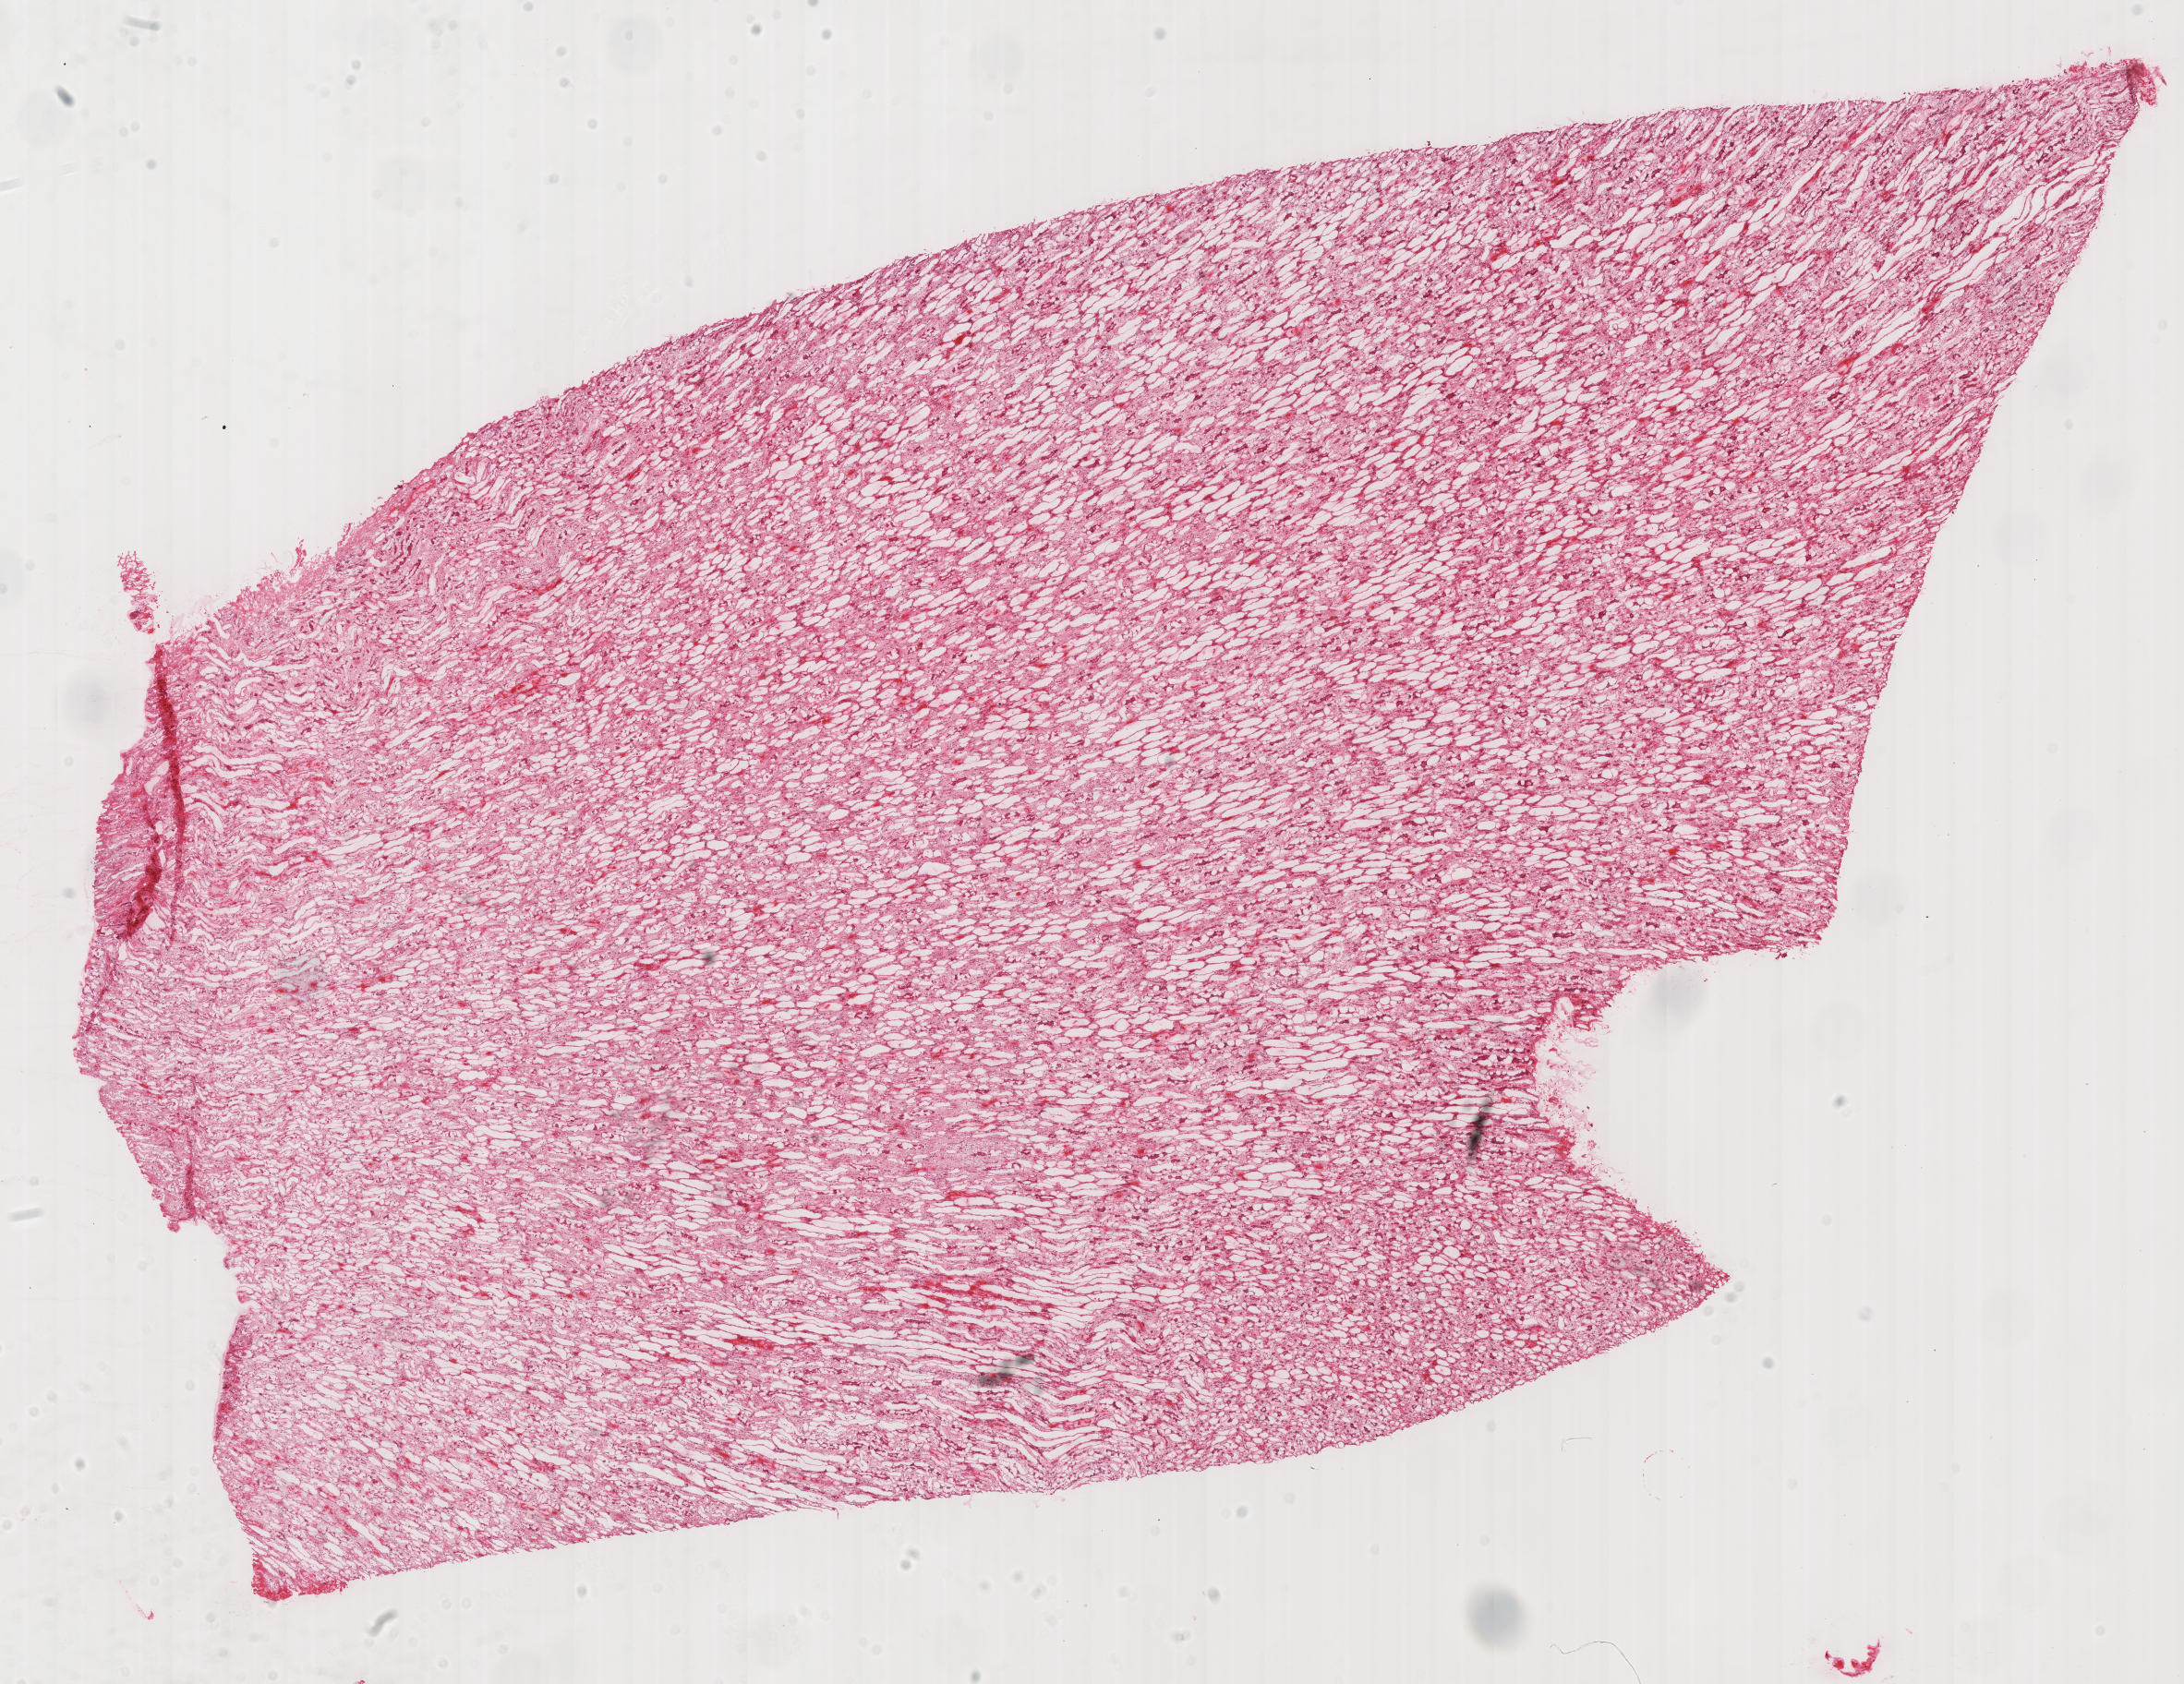
Whole-slide histology image, H&E-stained, low-resolution overview of the scanned area, about 18.6 x 14.3 mm. Frozen section from the top of the tissue portion. Solid tissue normal (non-tumour tissue) sample from the kidney. Female patient; age at initial diagnosis 38 years. Infiltration values recorded for this section: lymphocyte infiltration 0%, monocyte infiltration 0%, neutrophil infiltration 0%.
This section: solid tissue normal sample (biorepository sample class). Patient diagnosis: Renal cell carcinoma, chromophobe type.